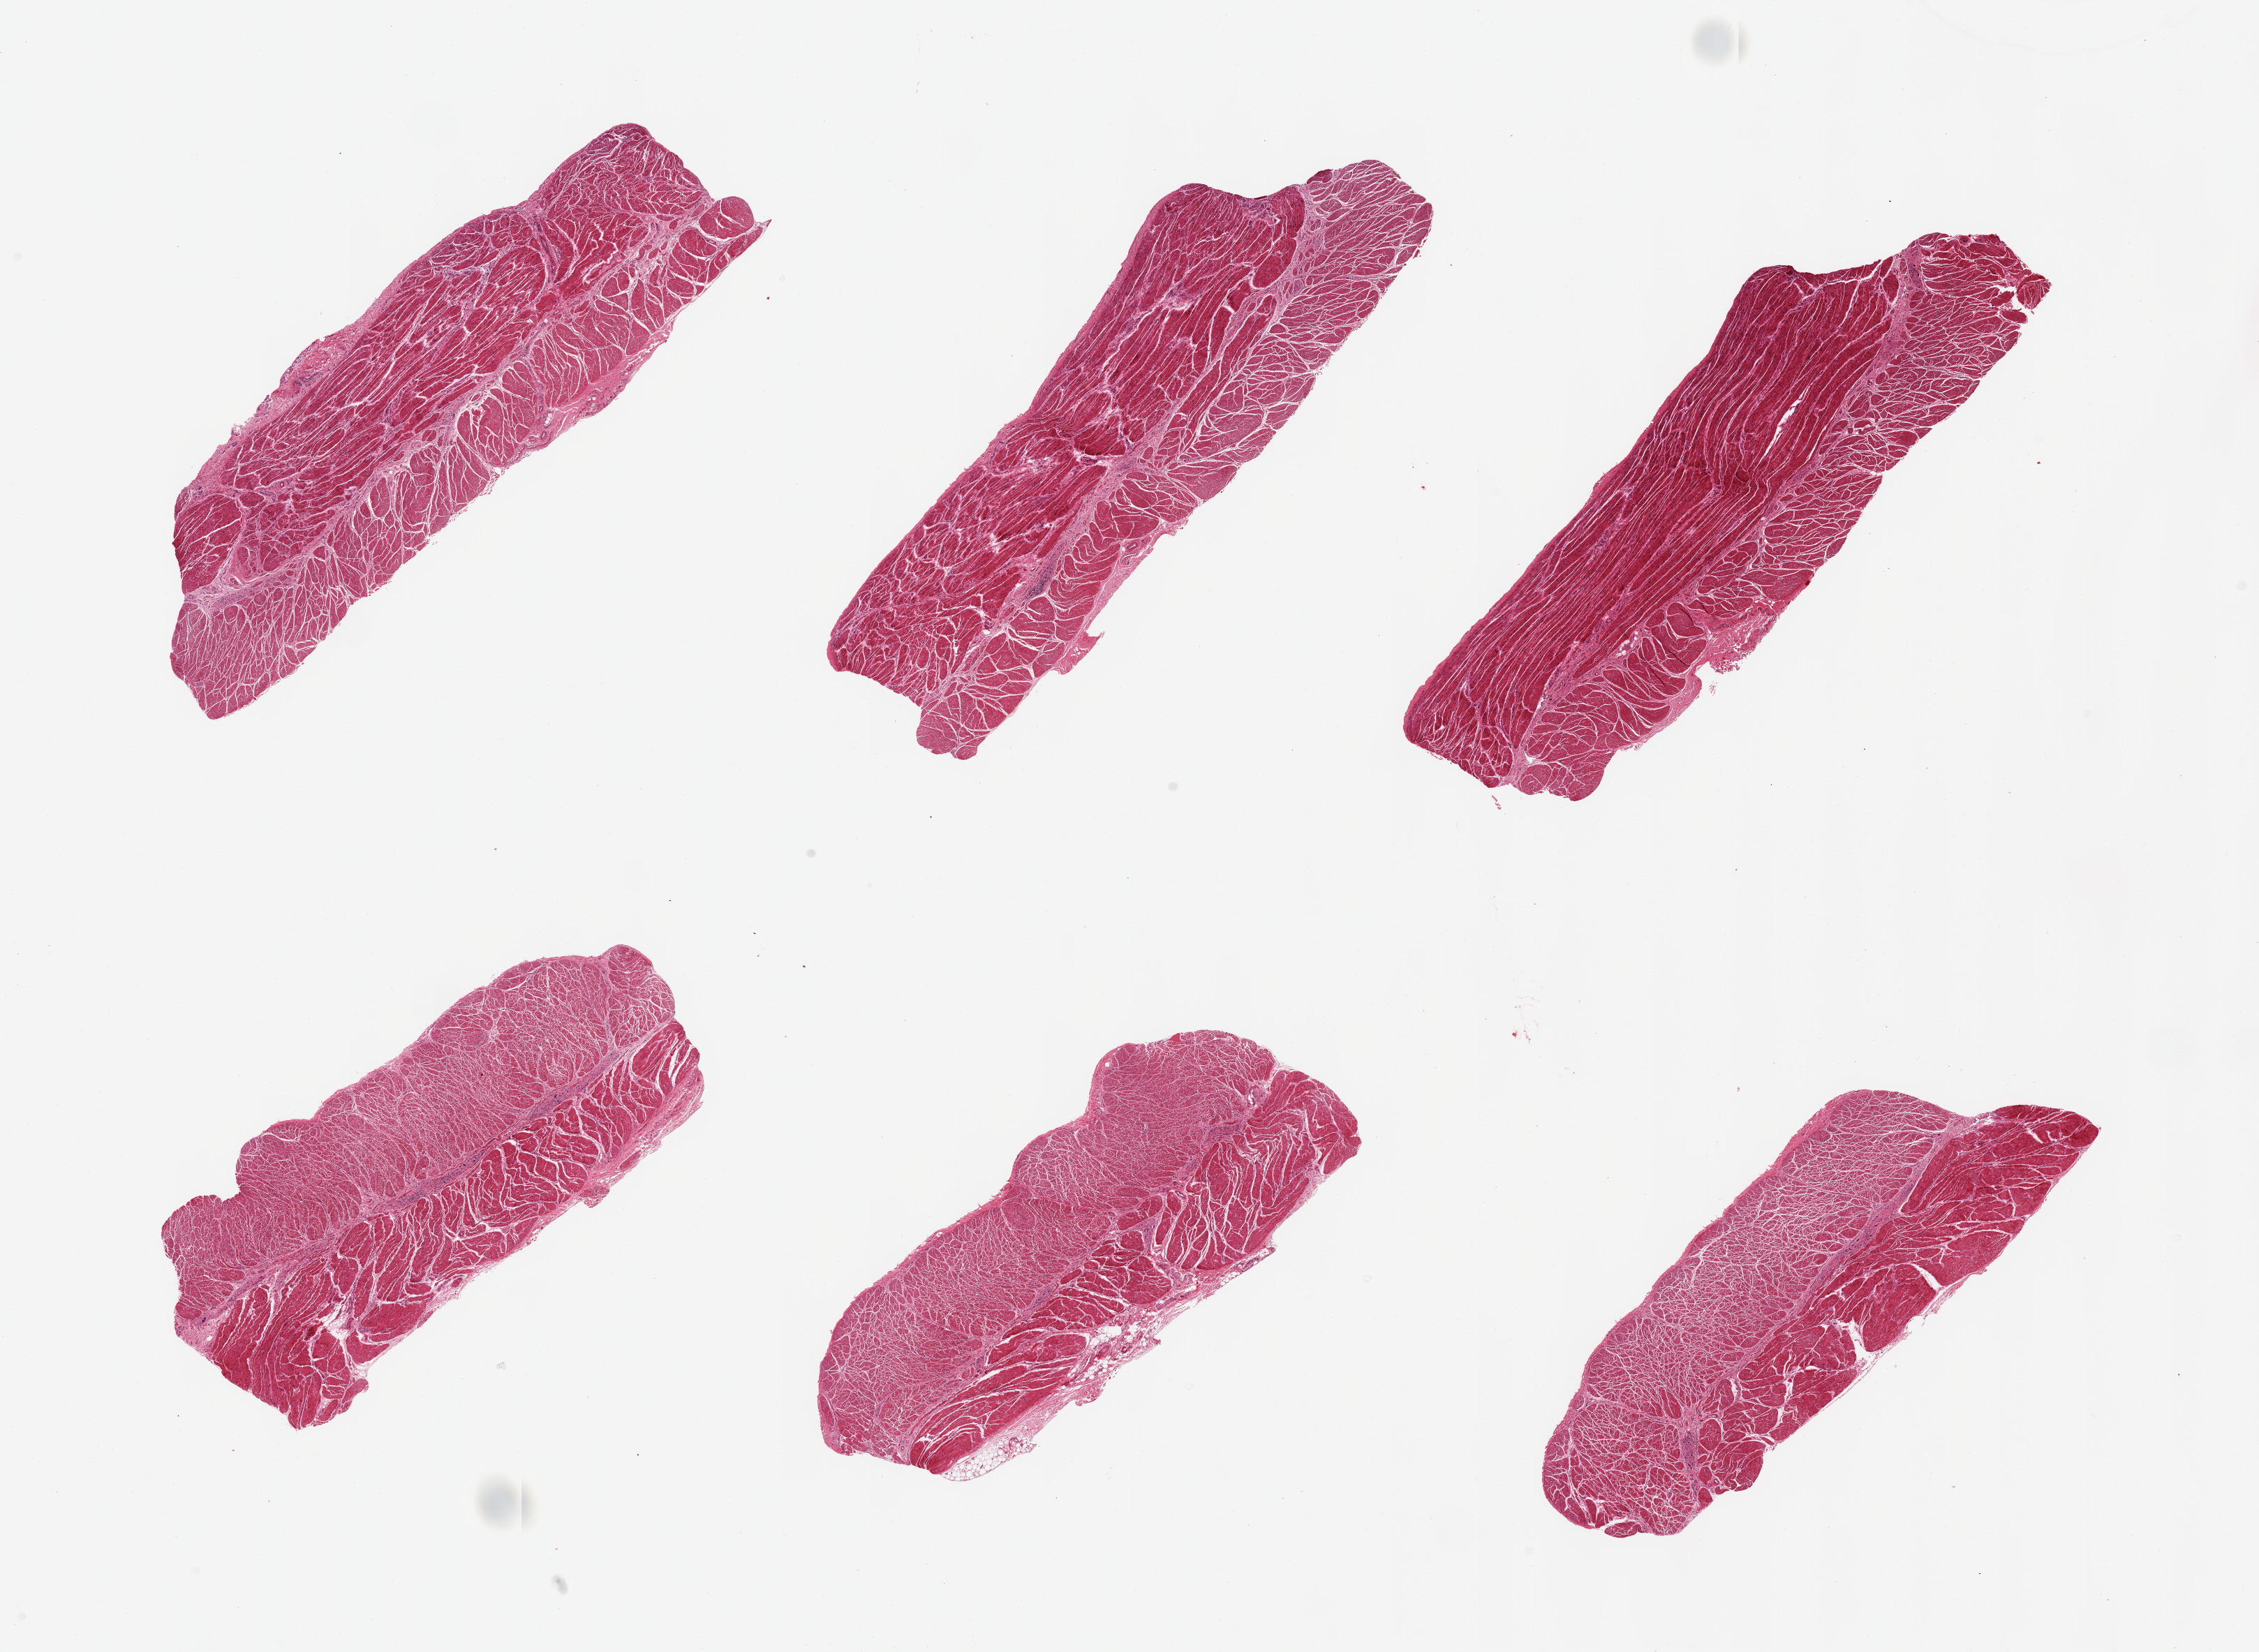
Whole-slide image, hematoxylin and eosin (H&E) stain, low-resolution overview of the scanned area, about 25.6 x 18.7 mm (acquisition: 20x scan), PAXgene-fixed paraffin-embedded (PFPE) section, section of esophageal muscle (target tissue), donor tissue sample. Male donor.
Pathologist's review note for this sample: 6 pieces; well dissected; lymphoid aggregates around ganglion cells.